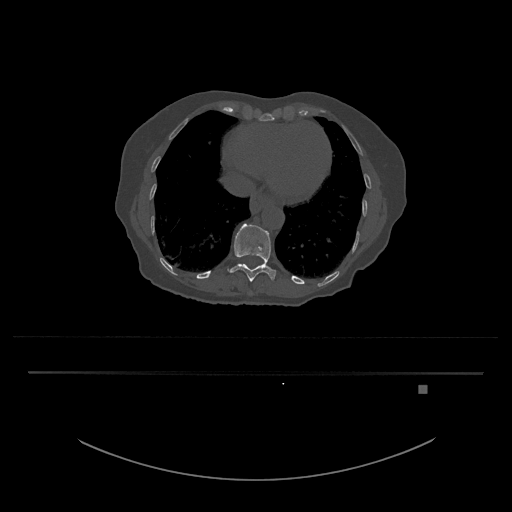
CT including the spine, one axial slice. Position 664 of 797 along the scan axis. Reconstruction kernel Br40s/3. 120 kVp. Bone window (W 1800 / L 400 HU). 0.5 mm slice thickness. 512 × 512 image matrix, field of view 500 × 500 mm. Patient: female, 57 years. Case-level facts recorded for this patient, not image findings: primary cancer: cervical.
Outlined on this slice (semi-automatically segmented with operator editing):
- T11 vertebra: bounding box [x1, y1, x2, y2] px = [228, 223, 276, 282]